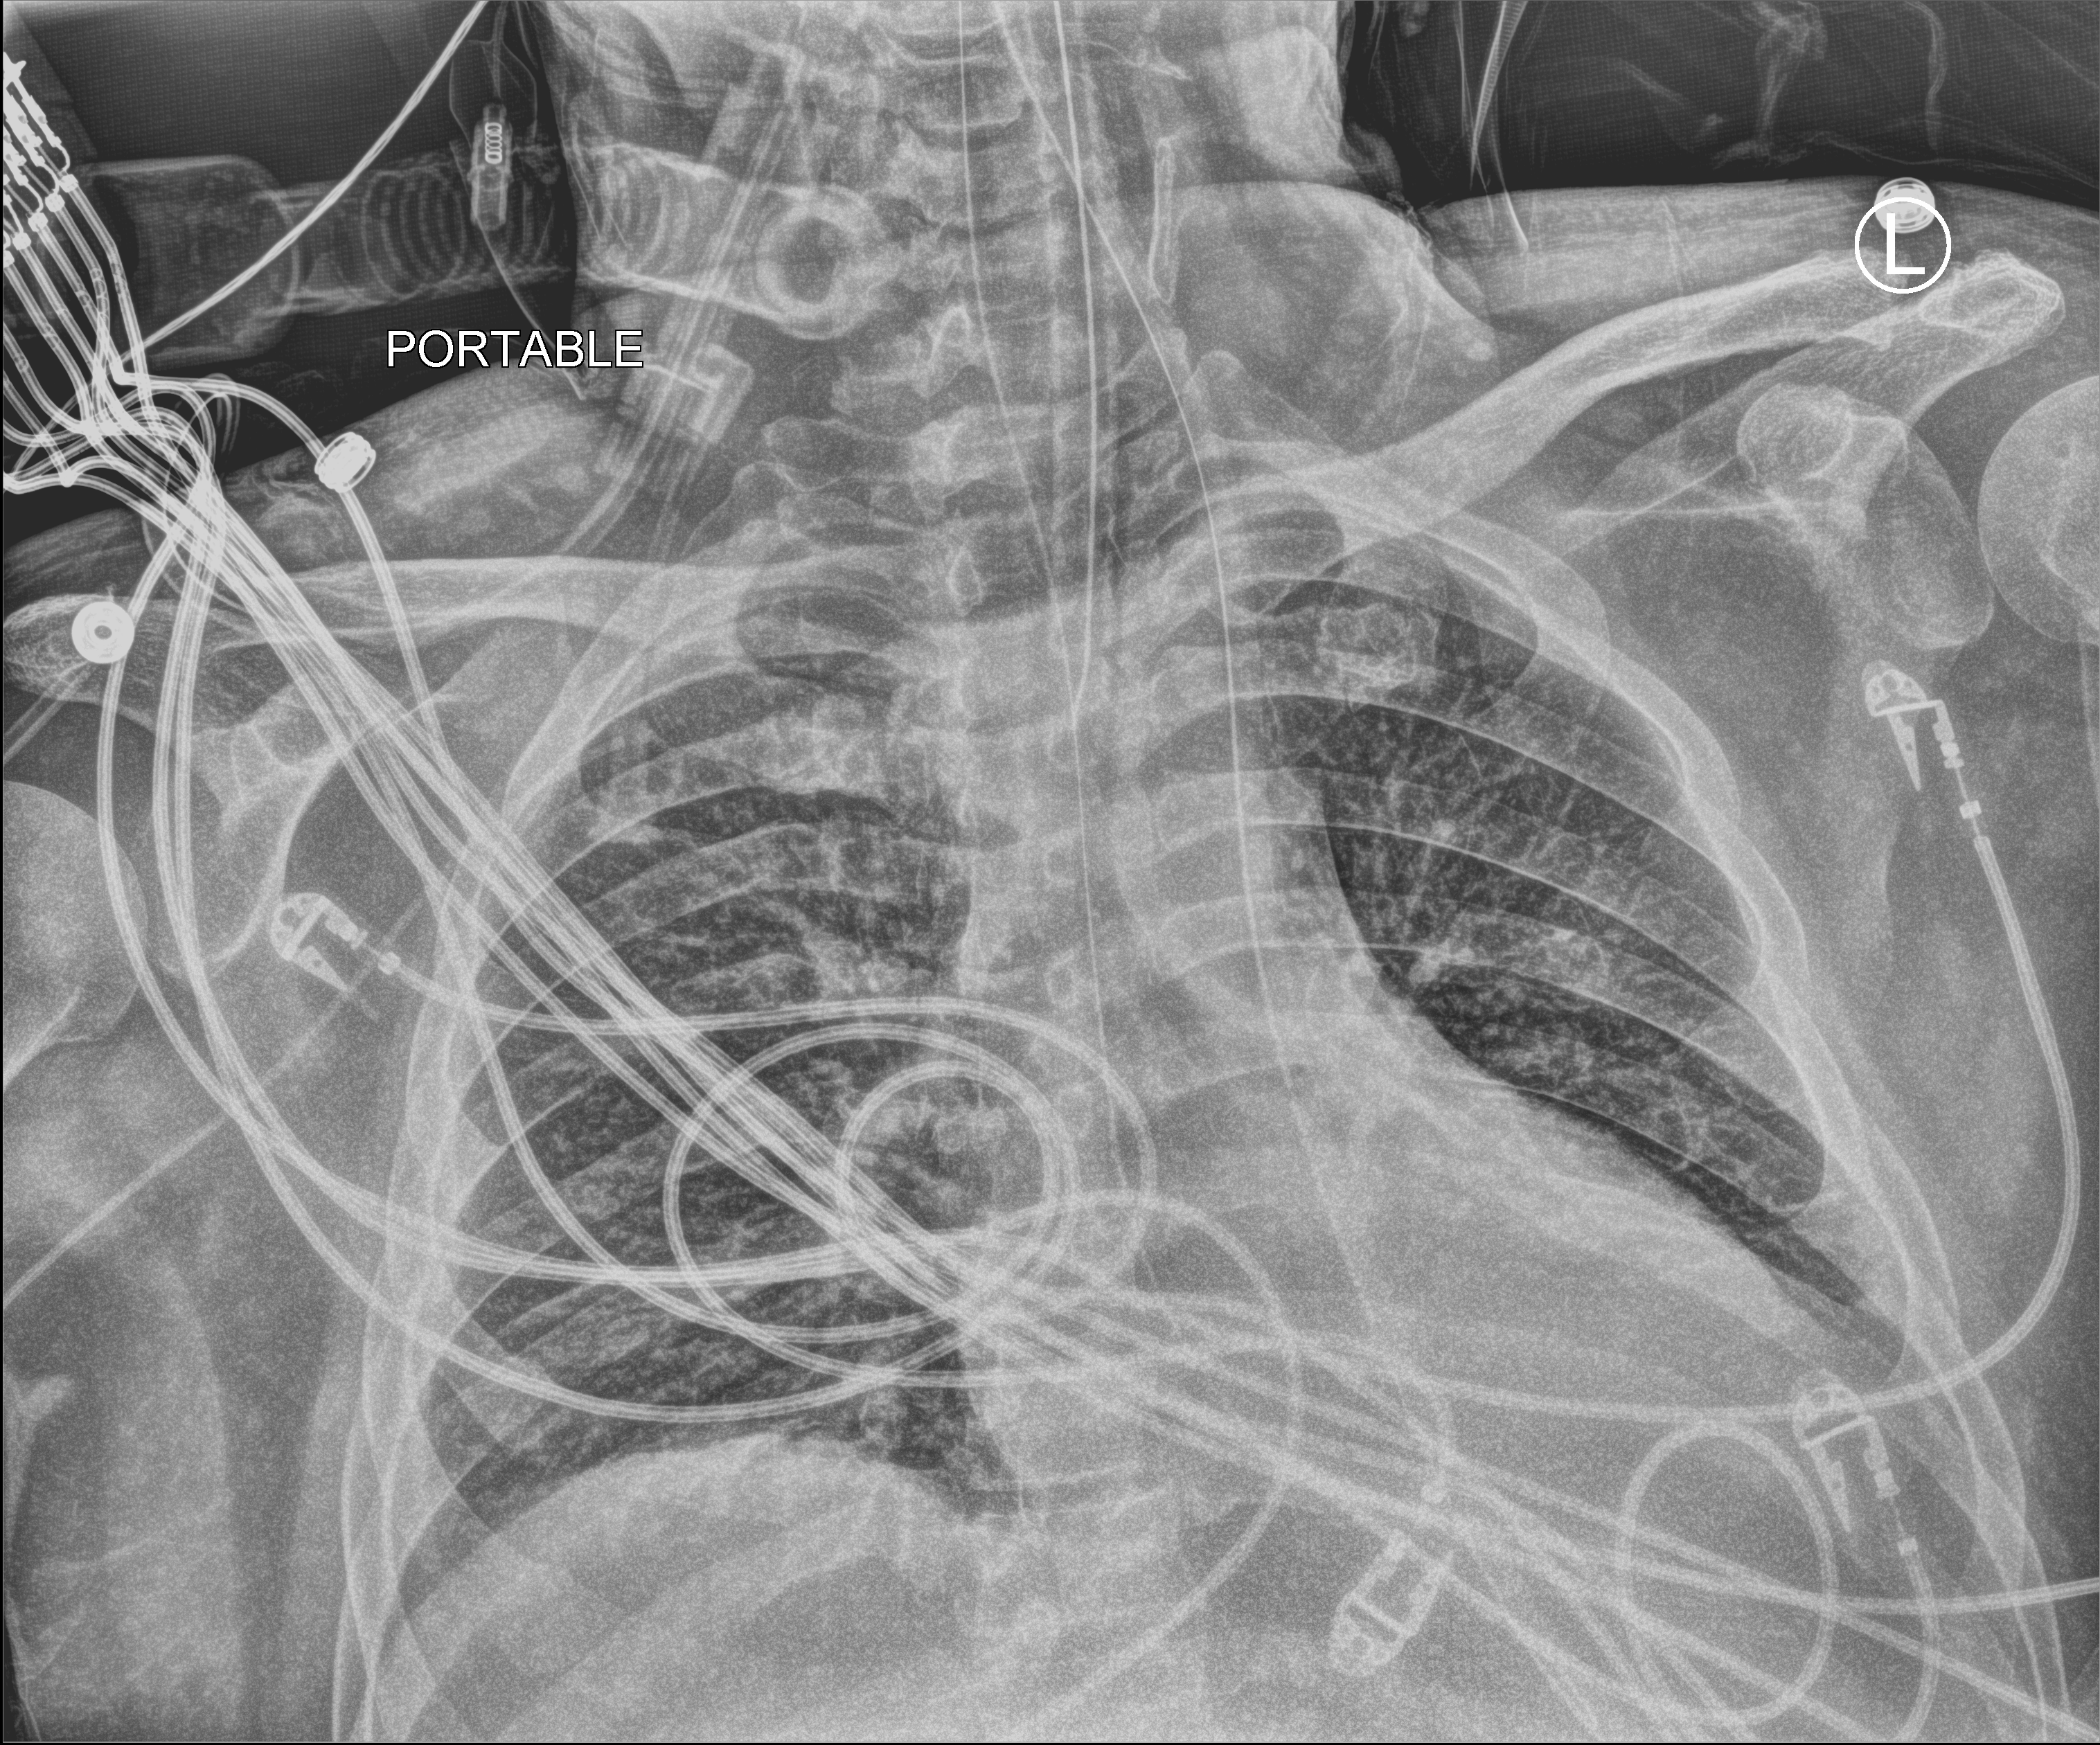
Portable chest radiograph; anteroposterior (AP) projection. Male patient hospitalised with COVID-19, age 18–59 years.
From the hospital-stay record, not from the radiograph (when in the stay this image was taken is not recorded): mechanically ventilated during this hospital stay: yes; admitted to intensive care during this hospital stay: yes.